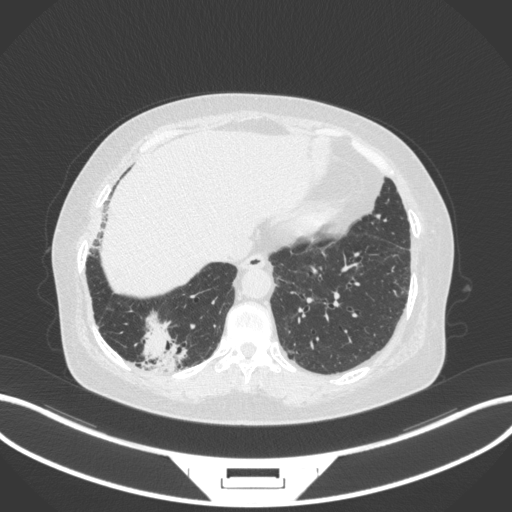
Chest CT, one axial slice; slice 36 of 303 in the series (ordered by position); 120 kVp; lung window (W 1500 / L -600 HU); 1 mm slice thickness; 512 × 512 image matrix. Patient: female, 65 years. From the clinical record (not read from this slice): clinical TNM (as recorded): T2b N1 M0.
Outlined on this slice (bounding box drawn by a radiologist):
- lung tumour (recorded histology: adenocarcinoma): bounding box <137,307,186,373> (left, top, right, bottom; pixels)